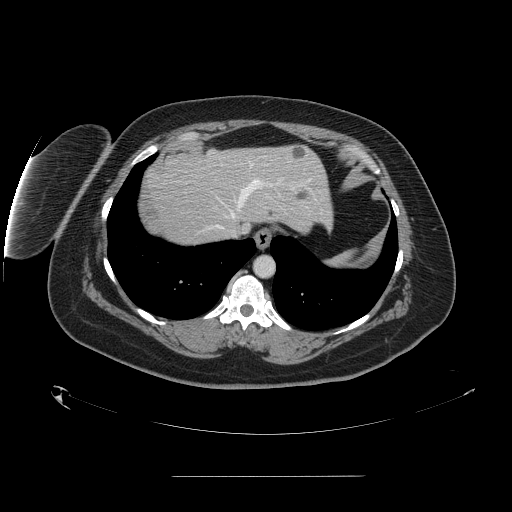
Contrast-enhanced abdominal CT, one axial slice. 120 kVp. Soft-tissue window (W 400 / L 40 HU). 512 × 512 image matrix, field of view 495 × 495 mm. Female patient, age 52 years. From the clinical record (not read from this slice): diagnosis: colorectal cancer liver metastases, imaged before liver resection; multiple liver metastases: yes; largest metastasis: 3.5 cm.
Outlined on this slice (manually delineated by an expert):
- hepatic veins: box from (x=216, y=162) to (x=282, y=237) px
- liver: (x=146, y=145)–(x=331, y=245)
- planned liver remnant (the part of the liver to remain after resection): (x=174, y=145)–(x=332, y=228)
- liver metastasis: (x=298, y=193)–(x=307, y=199)
- liver metastasis: (x=291, y=148)–(x=307, y=159)